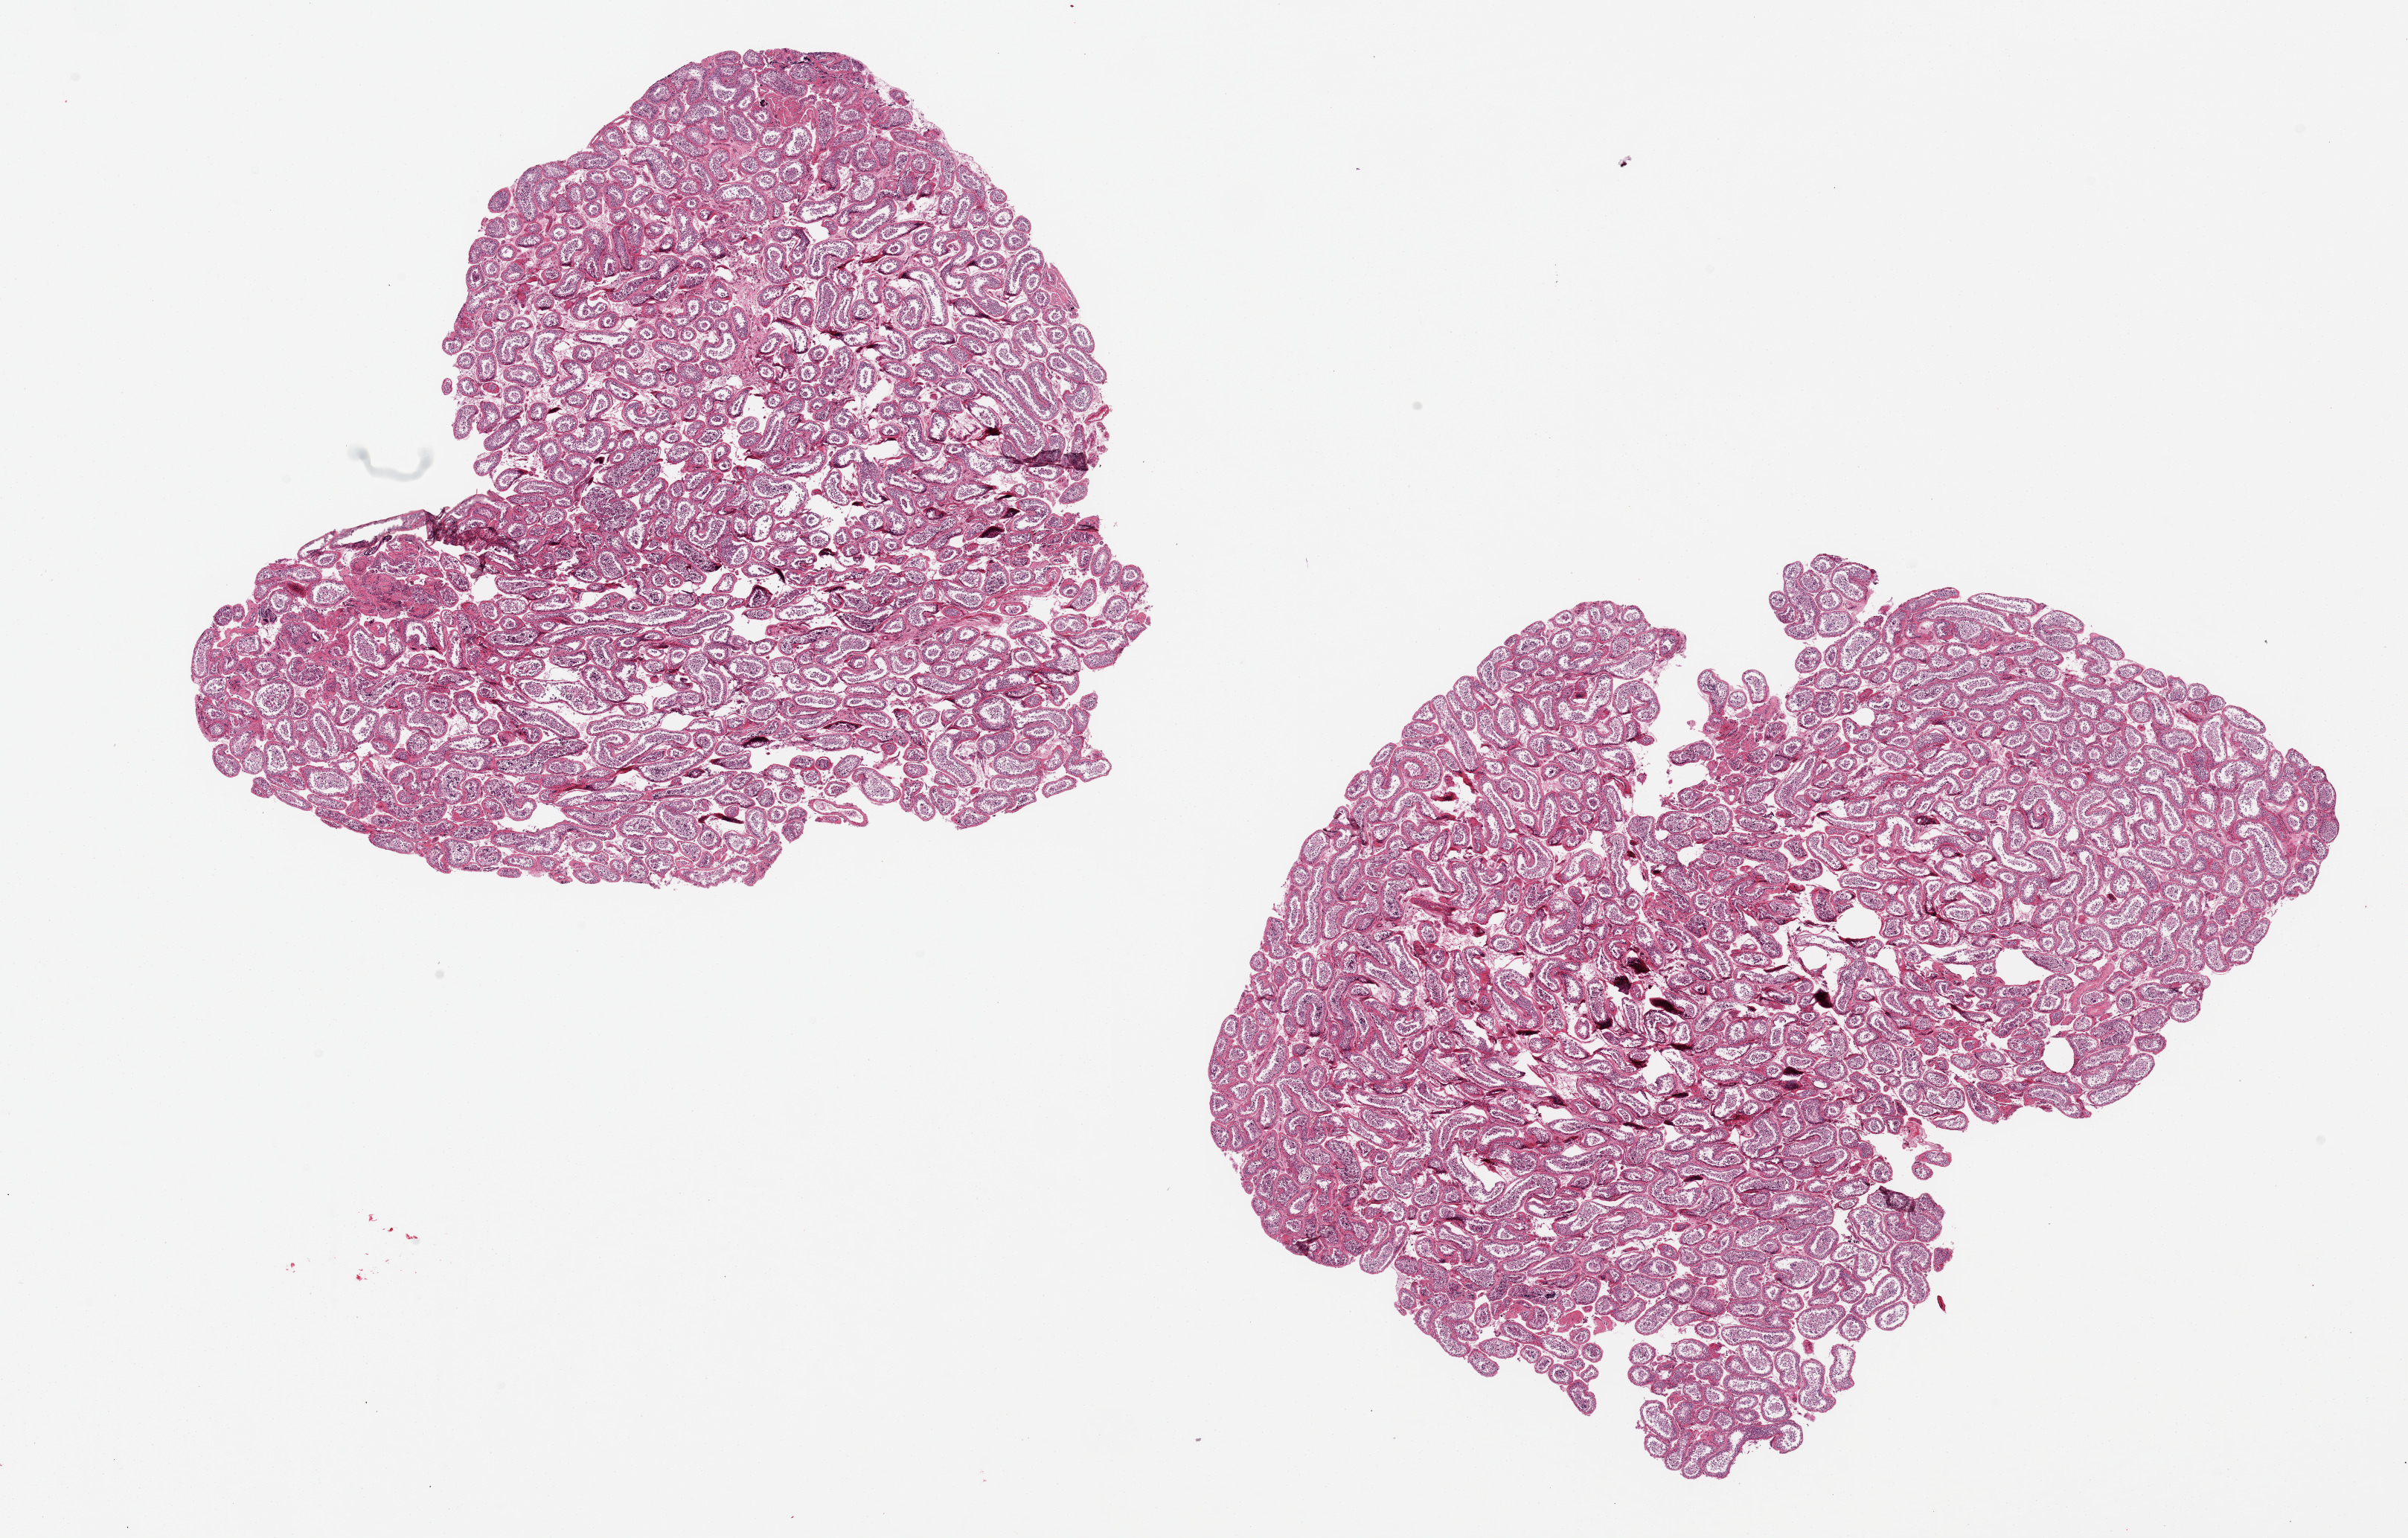
H&E whole-slide image, whole scanned area (about 25.6 x 16.3 mm) shown as a low-resolution overview. PAXgene-fixed, paraffin-embedded tissue. Section of testis (target tissue). Donor tissue sample. Male donor.
Pathologist's review note for this sample: 2 pieces 10x8 & 10x8 mm; slight decrease iin spermatogenesis.